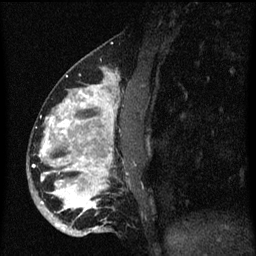
Breast MRI (dynamic contrast-enhanced), one sagittal slice. Dynamic contrast-enhanced series, image 2 of 3 at this slice position (ordered by acquisition). 1.5 T. TE 4.2 ms, TR 8.4 ms. 2 mm slice thickness. 256 × 256 image matrix. Female patient, age 34 years. Case-level facts recorded for this patient, not image findings: setting: breast cancer imaged before/during neoadjuvant chemotherapy; receptor status: HR-positive, HER2-negative.
Outlined on this slice (semi-automatic segmentation, software-assisted and operator-edited):
- analysis volume of interest (the breast-tissue region the enhancement analysis was run in; not a lesion): box from (x=28, y=58) to (x=137, y=237) px
- tumour enhancement mask (voxels above the 70 % enhancement threshold inside the analysis volume of interest): (x=40, y=74)–(x=117, y=231)